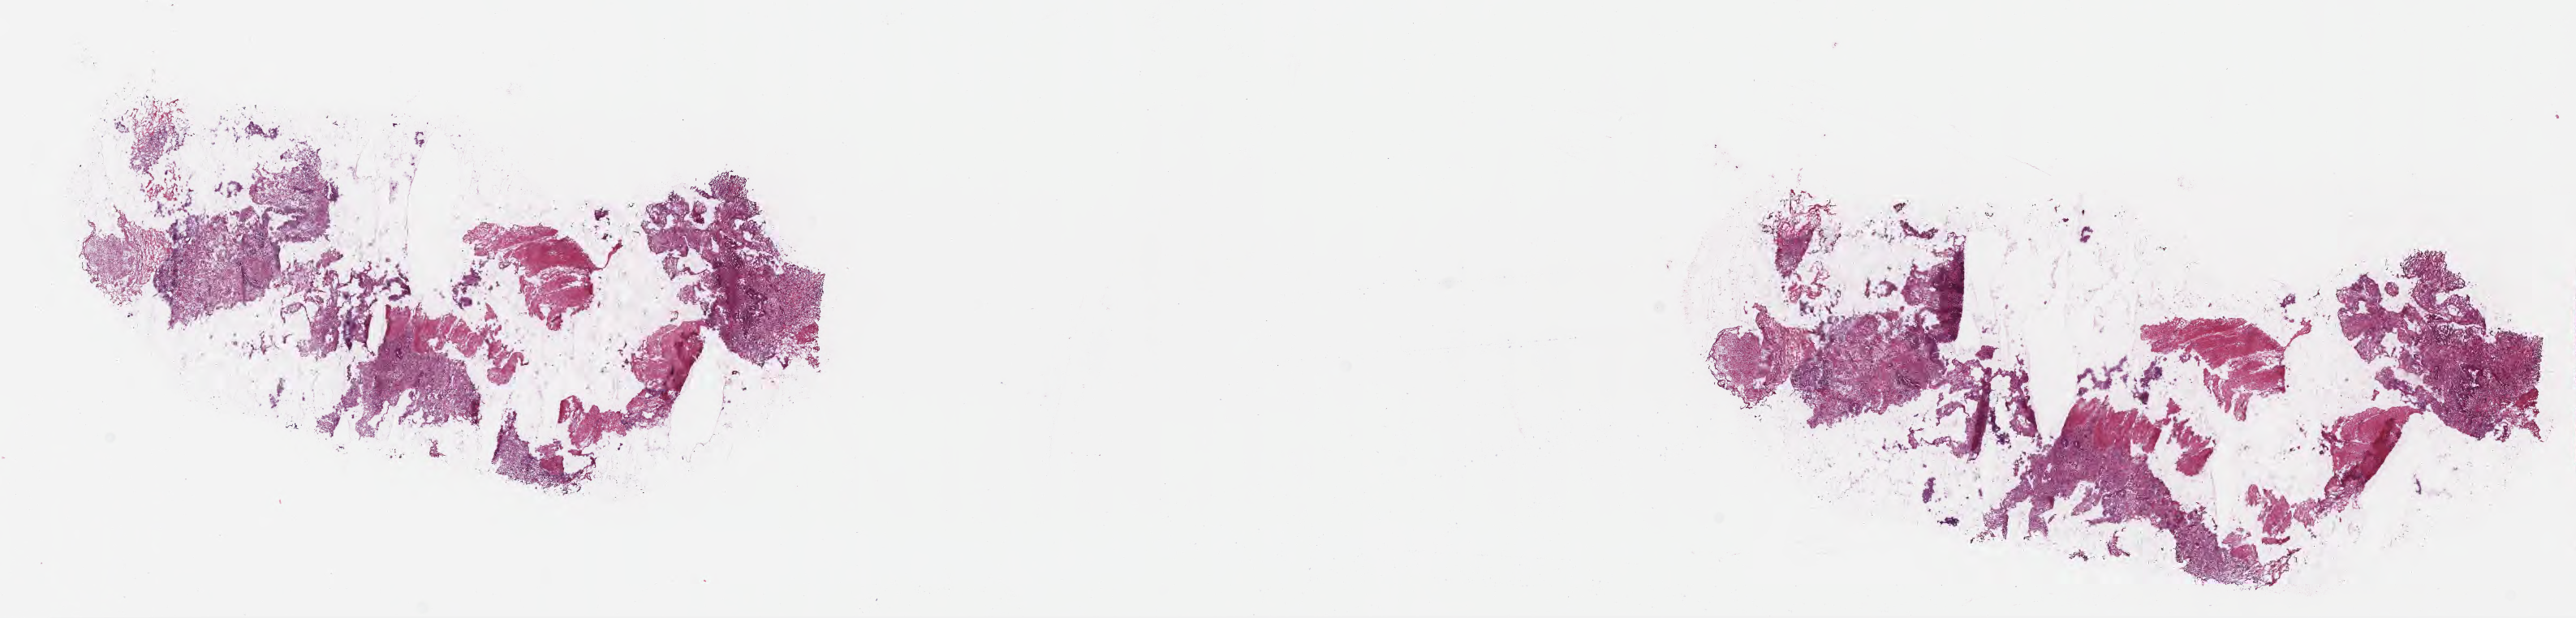
H&E whole-slide image — low-resolution overview of the scanned area, about 25.7 x 6.2 mm; frozen section; specimen: primary tumor; site: splenic flexure of colon. Female patient. Pathologist review of this section (percent, as recorded): tumor cells 70%, tumor nuclei 70%.
Diagnosis: Adenocarcinoma, NOS.